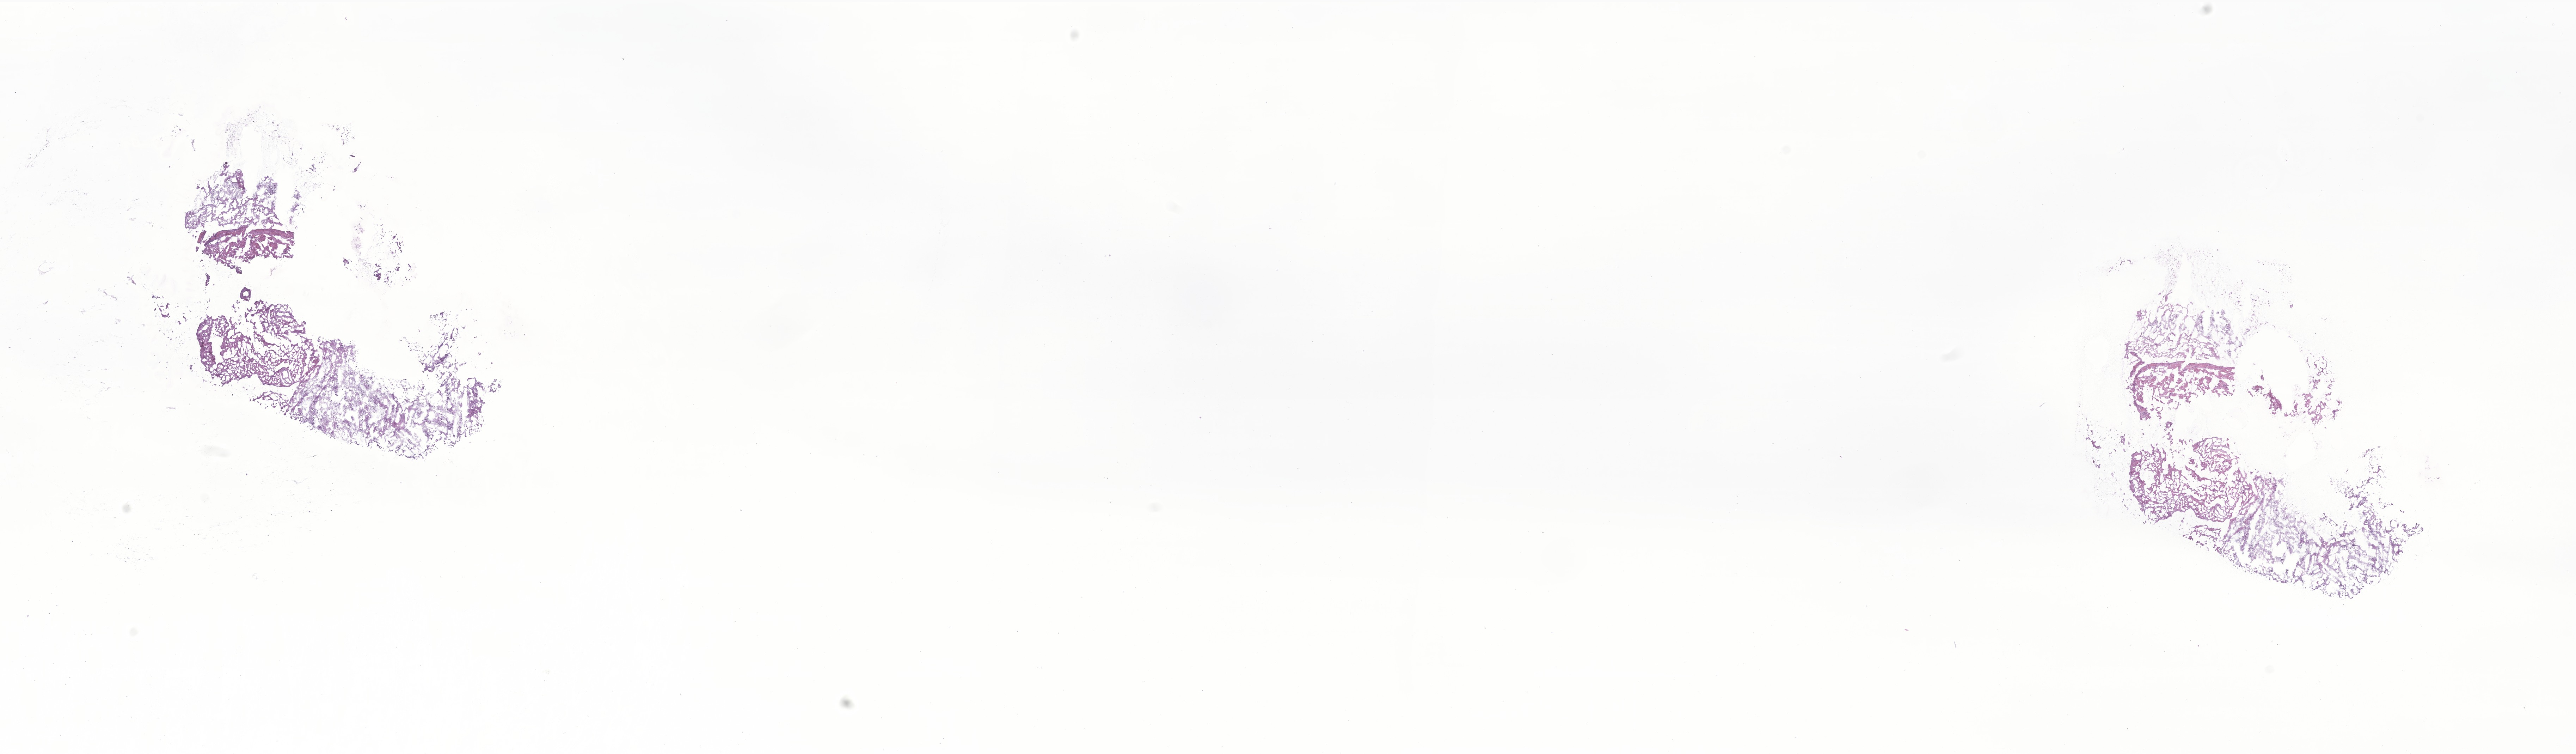
Whole-slide image, H&E stain of tumor tissue from the brain — shown as a low-resolution overview of the whole scanned area (about 30.8 x 9.0 mm), cryosection (OCT / tissue freezing medium). Female patient, age 118 months (9 years 10 months).
Diagnosis (ICD-O-3 morphology term): Pilocytic astrocytoma.